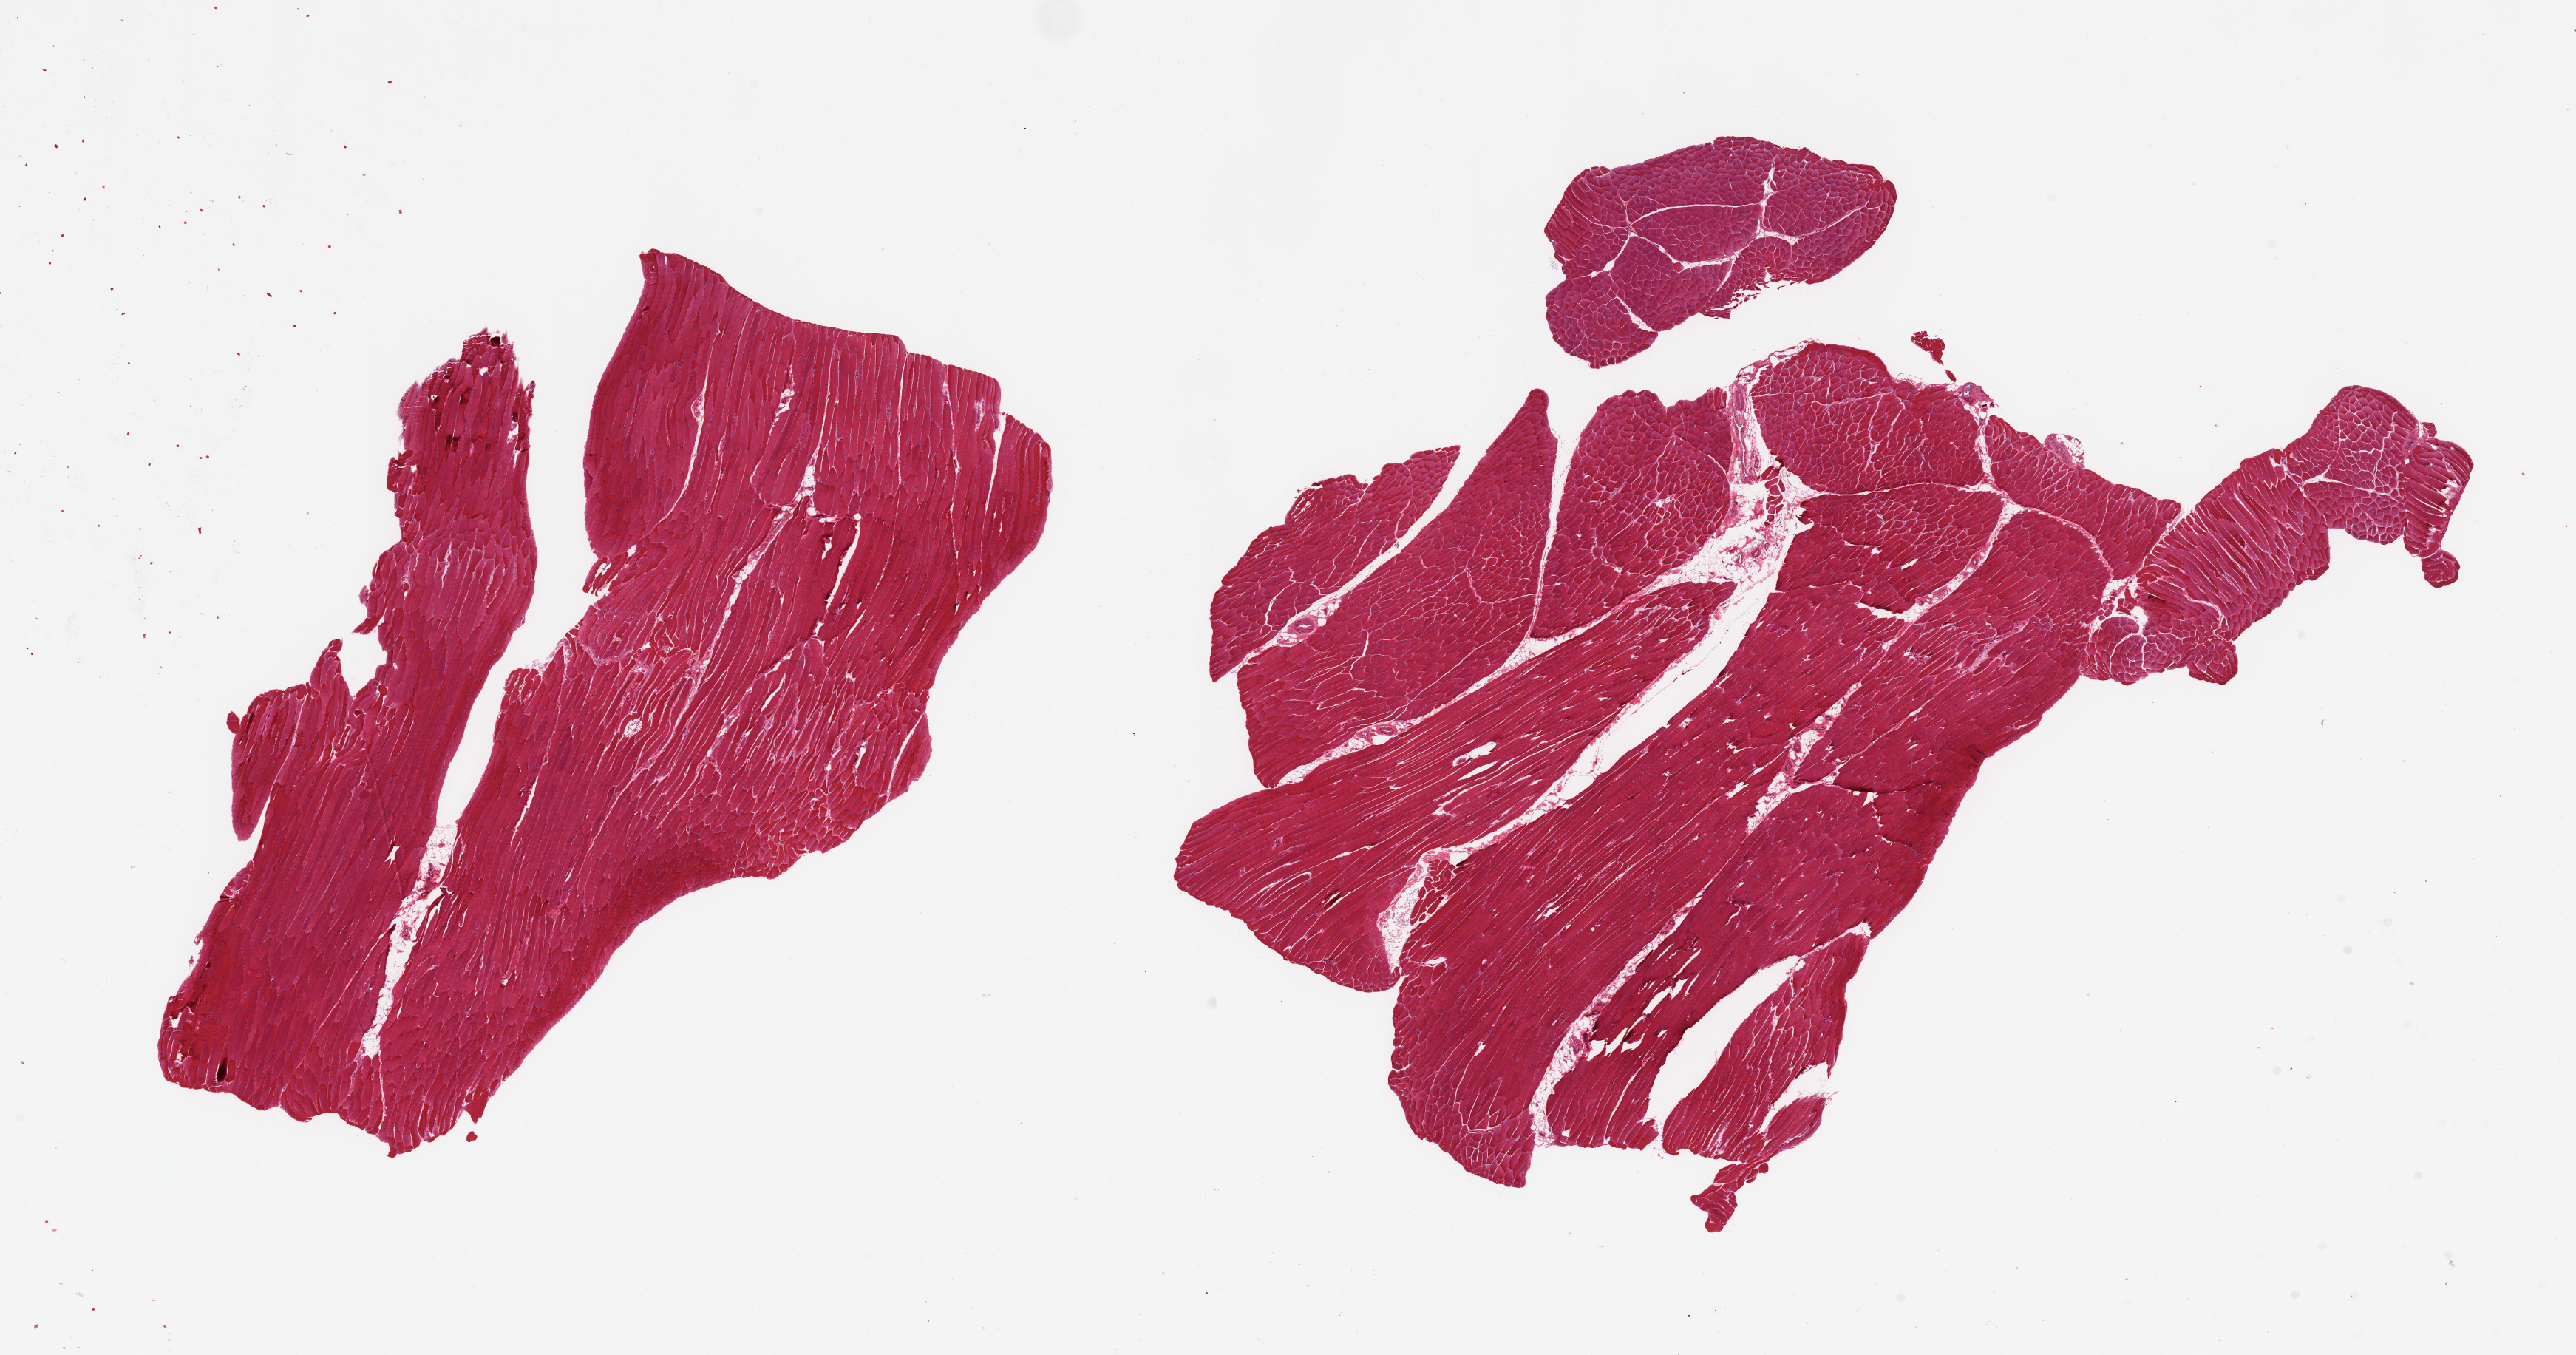
Digitized haematoxylin and eosin-stained section — a low-resolution overview of the entire scanned area, about 27.6 x 14.5 mm (acquisition: 20x scan); PAXgene-fixed paraffin-embedded (PFPE) section; section of skeletal muscle (target tissue); tissue donor sample. Donor: male.
- review note (as recorded): 2 pieces; fat <5%